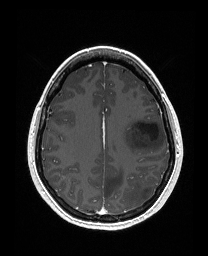
Brain MRI from a brain-tumour surgery series, one axial slice. Position 111 of 176 along the scan axis. T1-weighted post-contrast. 1 mm slice thickness. 208 × 256 image matrix, field of view 203 × 250 mm. From the clinical record (not read from this slice): histopathology: Astrocytoma; WHO grade: 3; IDH mutation: yes; tumour location: Left Frontal.
Structures marked on this image (manually delineated by an expert):
- tumour: bounding box [x1, y1, x2, y2] px = [122, 118, 165, 154]